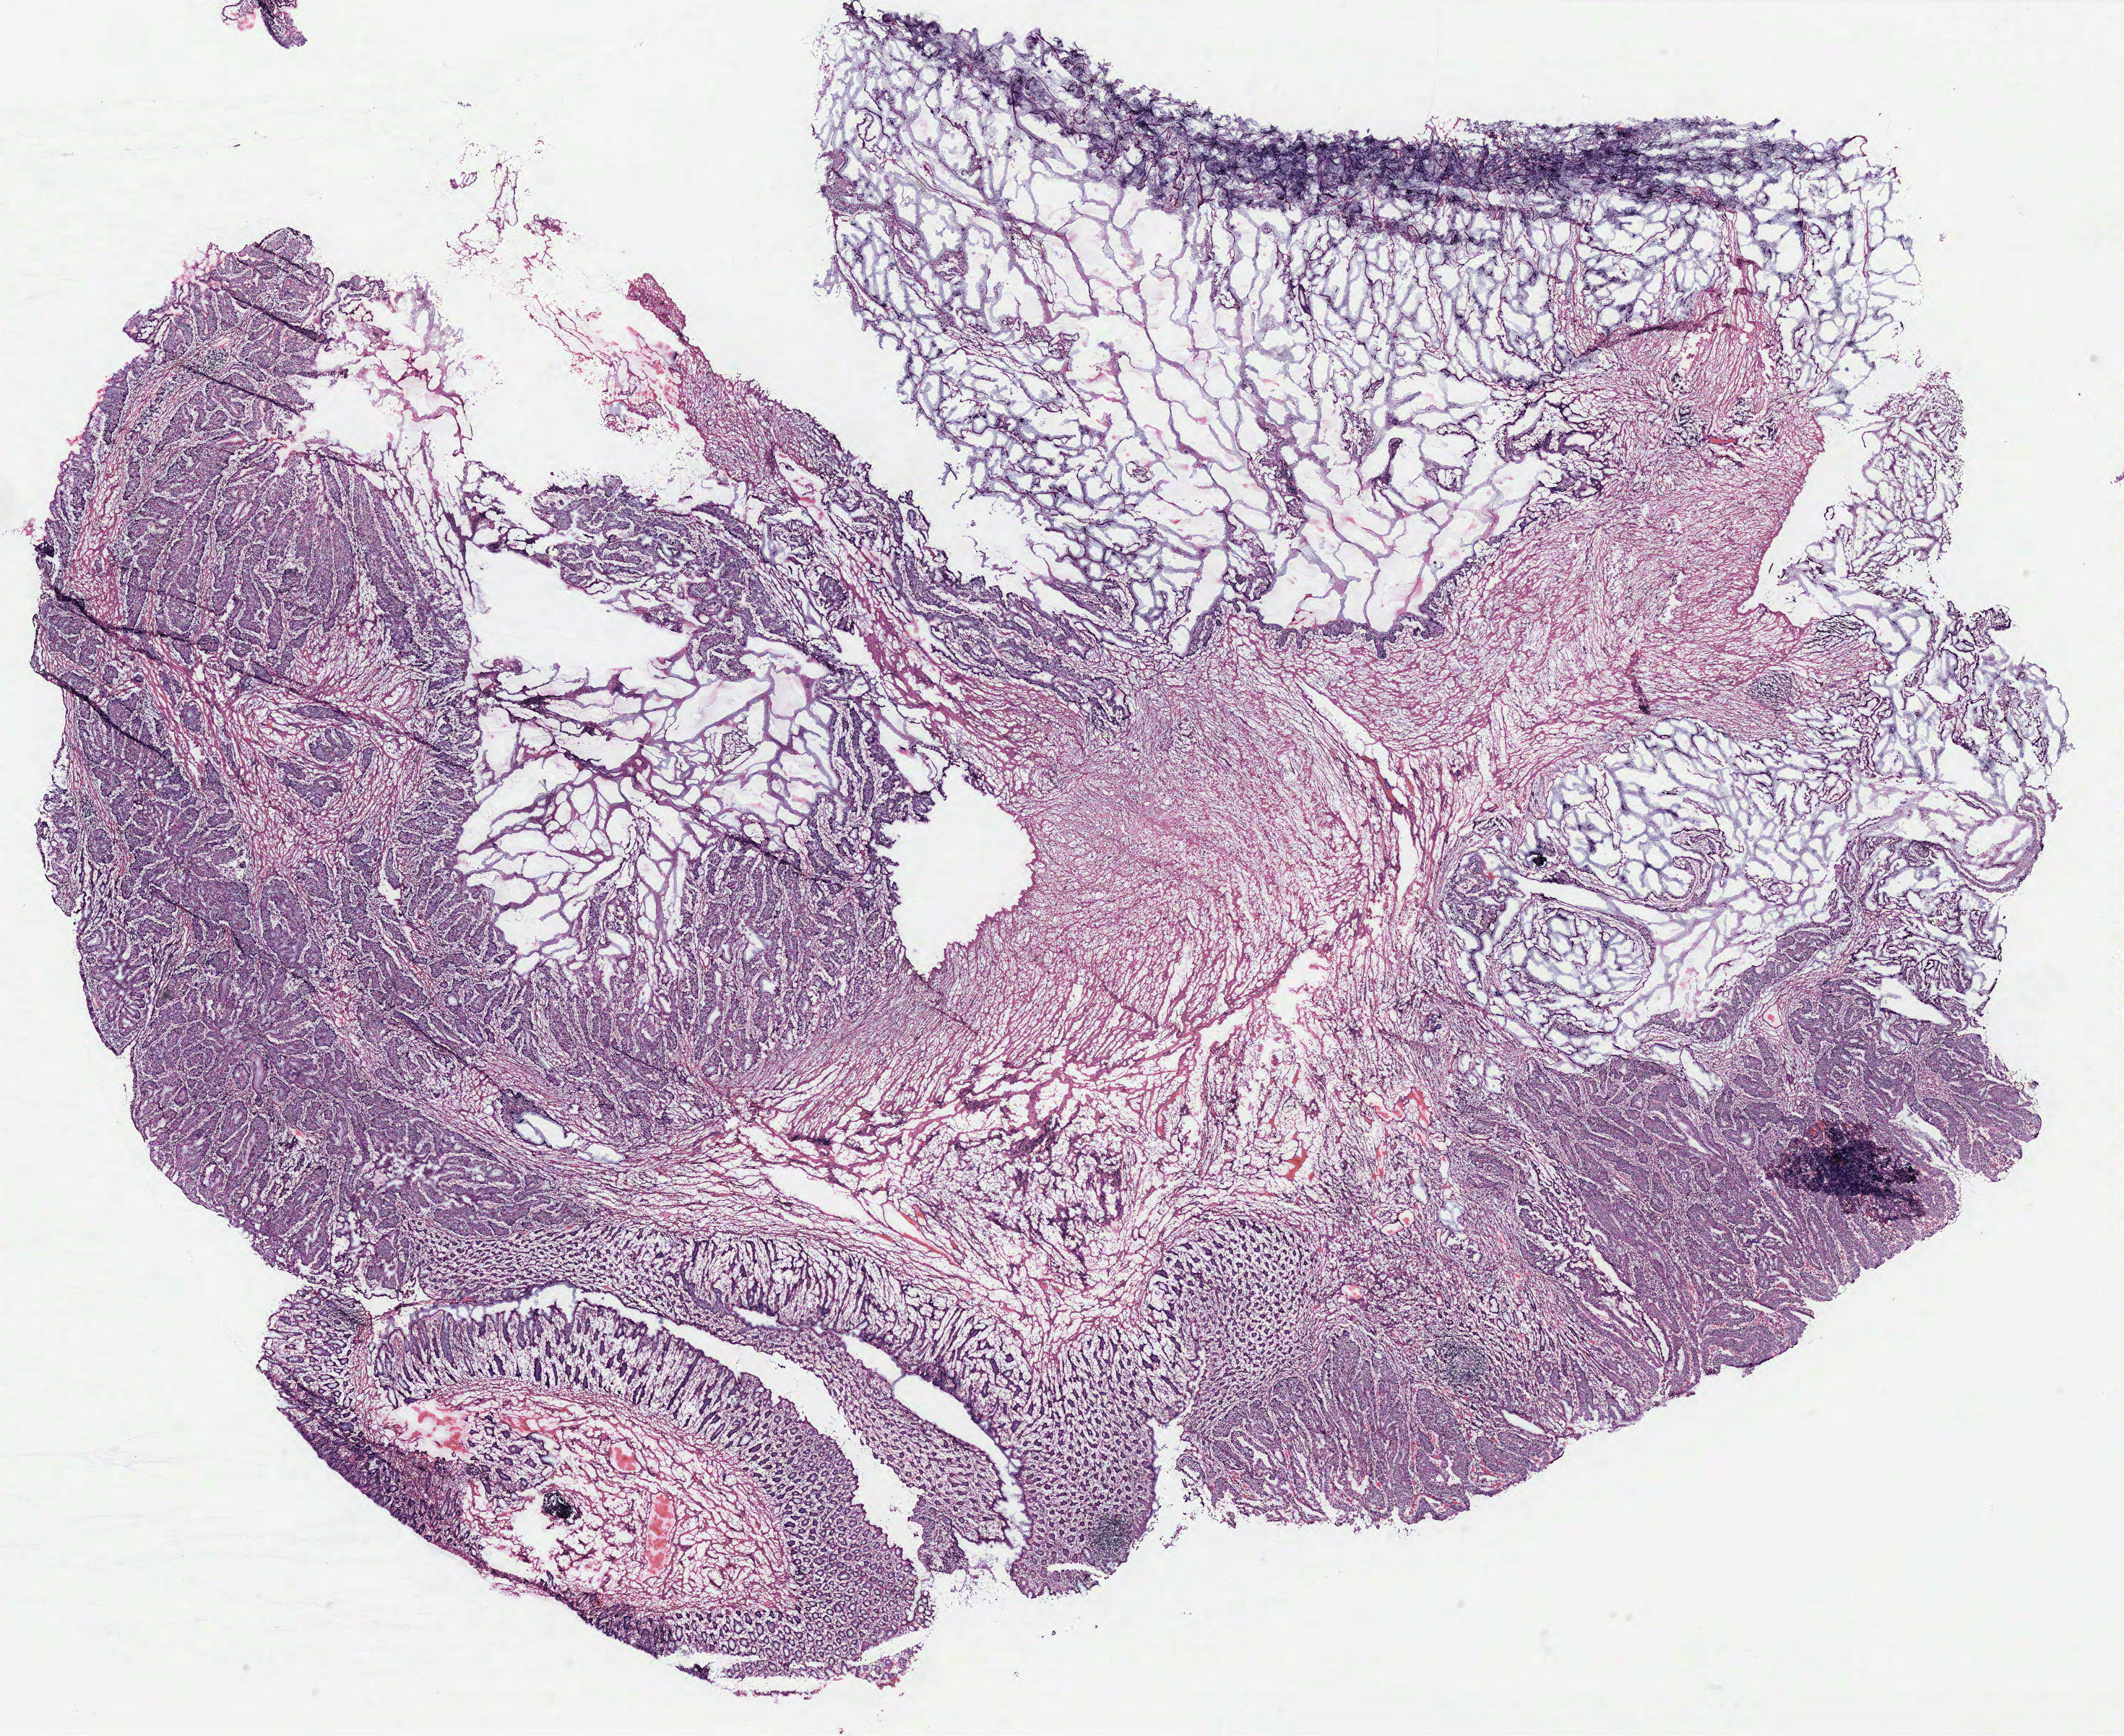
Digitized Hematoxylin and eosin (H&E) stained tissue section (whole slide) — whole scanned area (about 23.5 x 19.2 mm, acquisition: 40x scan) shown as a low-resolution overview. Colon, normal (non-tumour) tissue. Patient: female, age 66 years.
This section: normal (non-tumour) tissue from the same patient. Patient diagnosis: Adenocarcinoma, NOS.